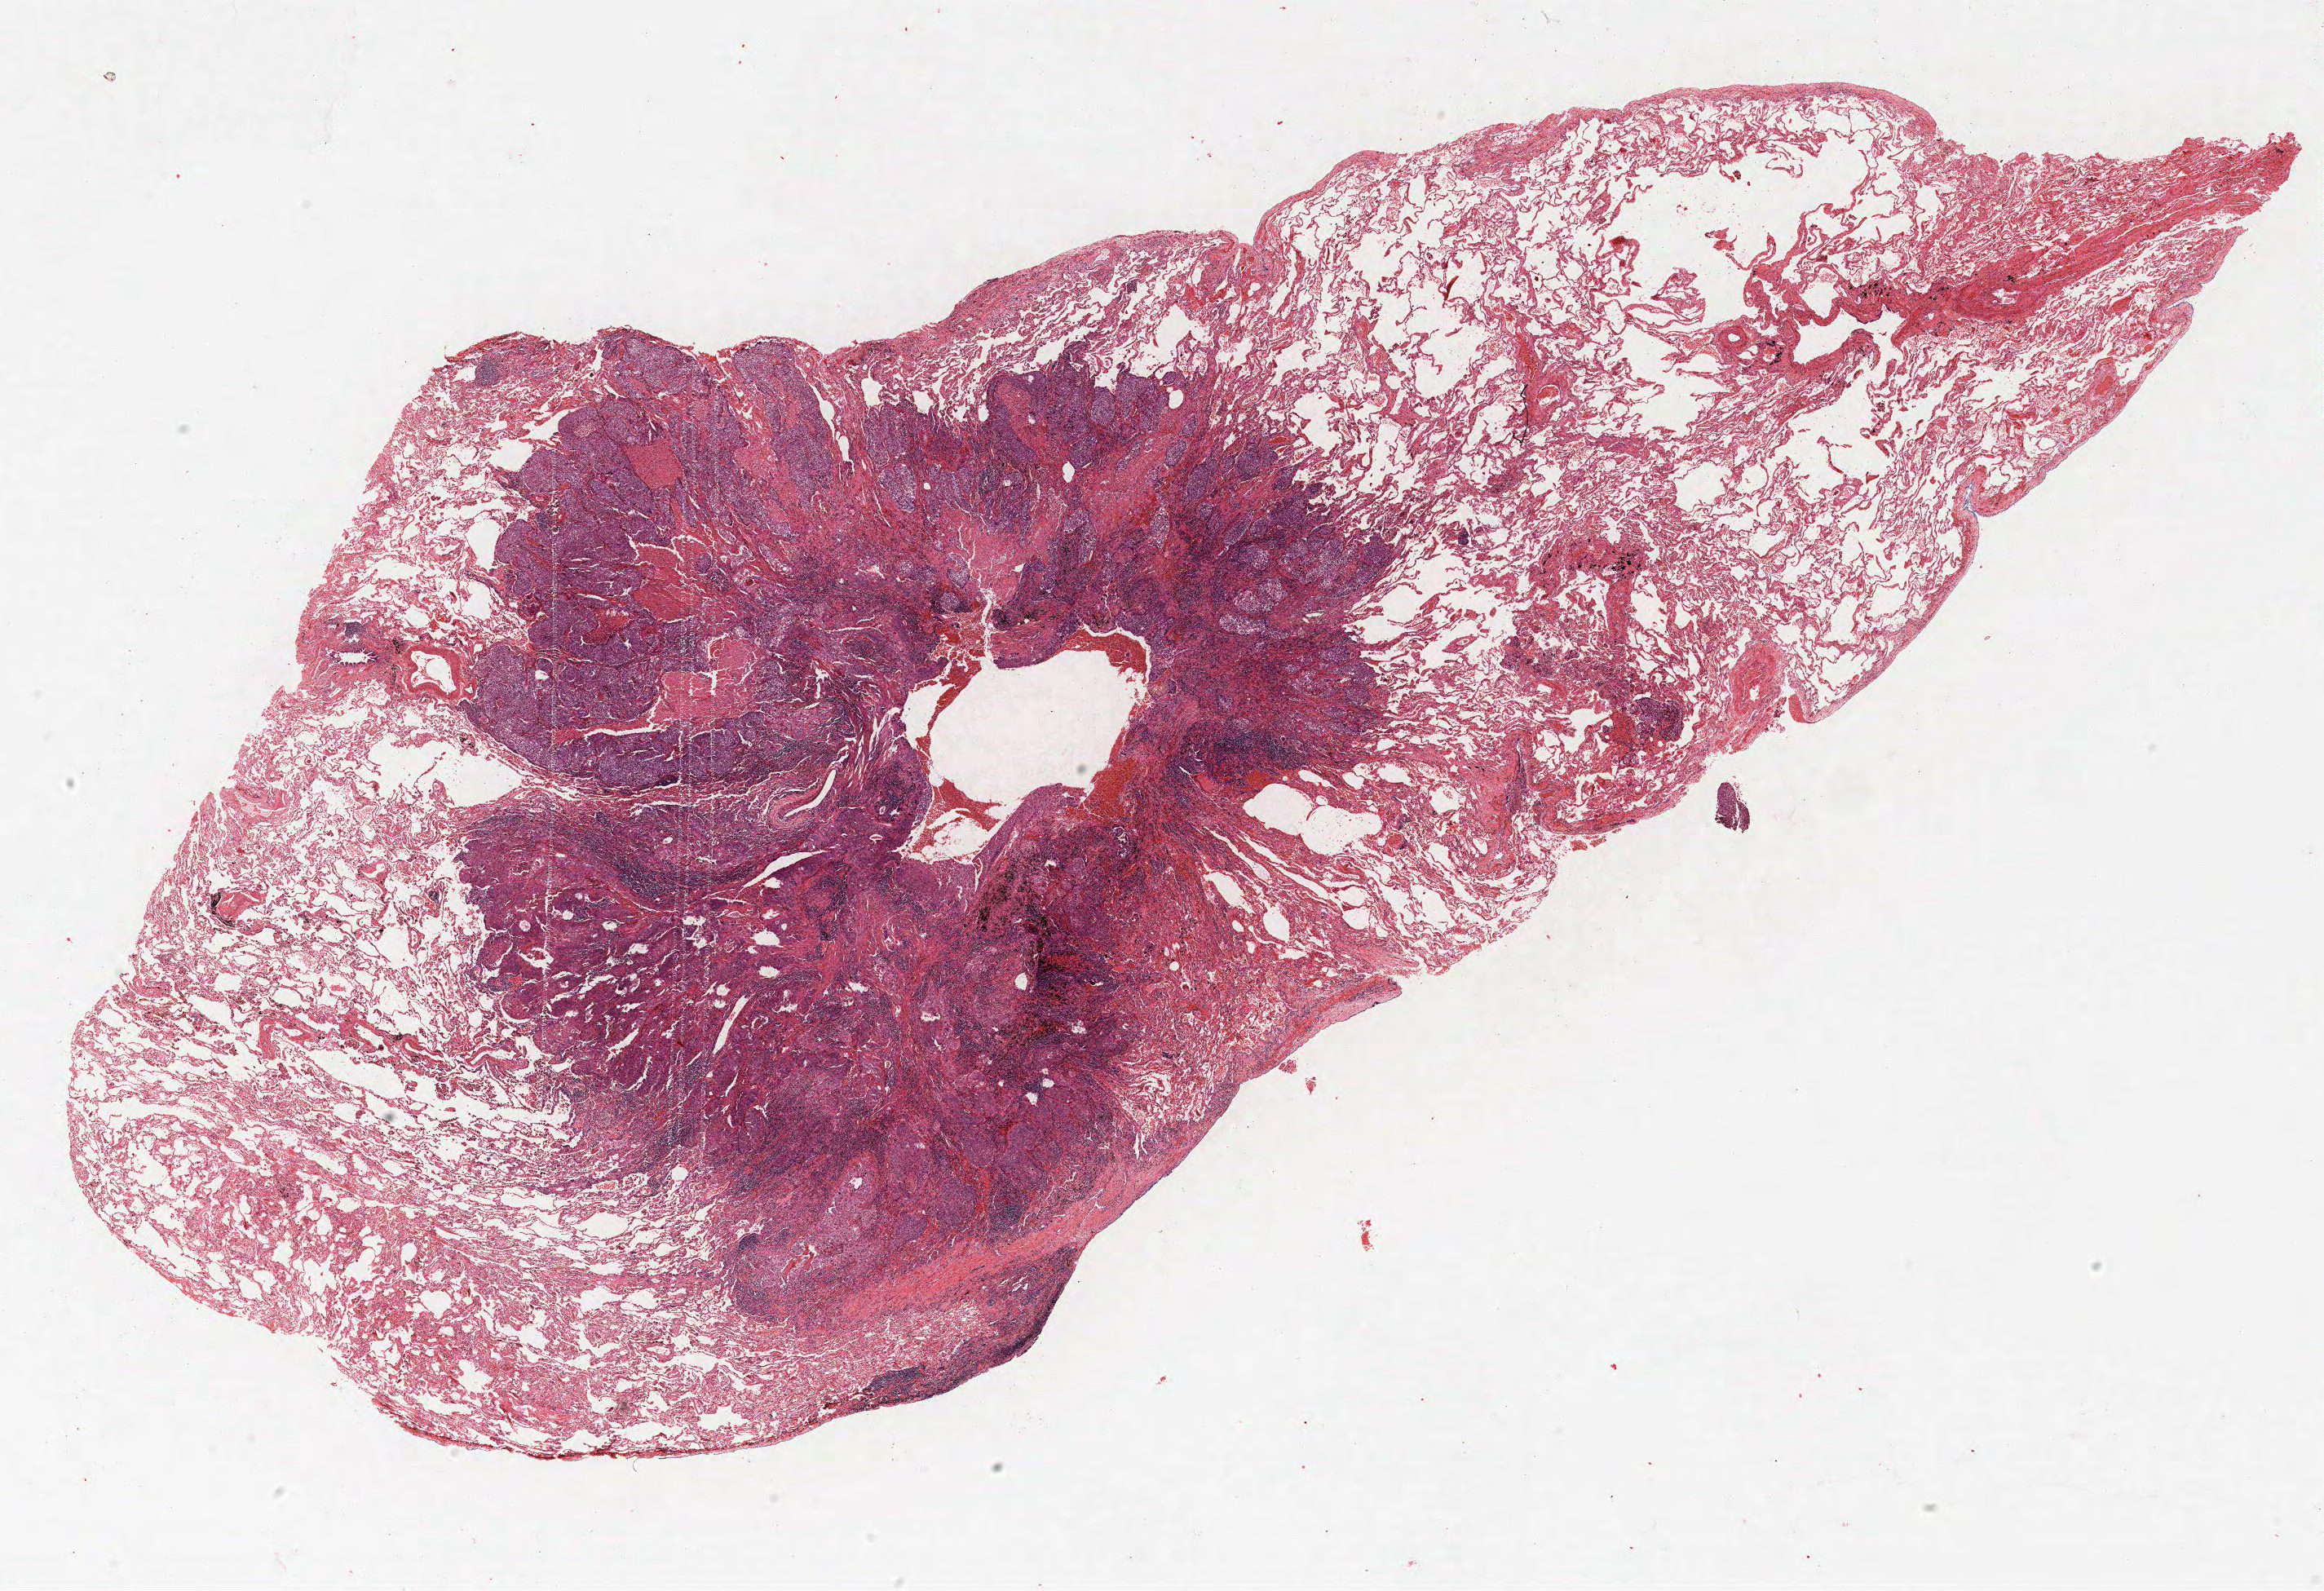
Whole-slide histology image, H&E, whole scanned area (about 22.8 x 15.6 mm, slide scanned at 40x) shown as a low-resolution overview; formalin-fixed paraffin-embedded (FFPE) section; lung tissue. Female, age 63 at enrolment. Current smoker at enrolment. Grade: moderately differentiated (G2).
* stage (AJCC 6th edition): IB
* tumour size (pathology): 15 mm
* participant's lung-cancer diagnosis: Squamous cell carcinoma, NOS
* primary tumour location (clinical record): left lower lobe
* ICD-O-3 topography: lower lobe of lung (C34.3)